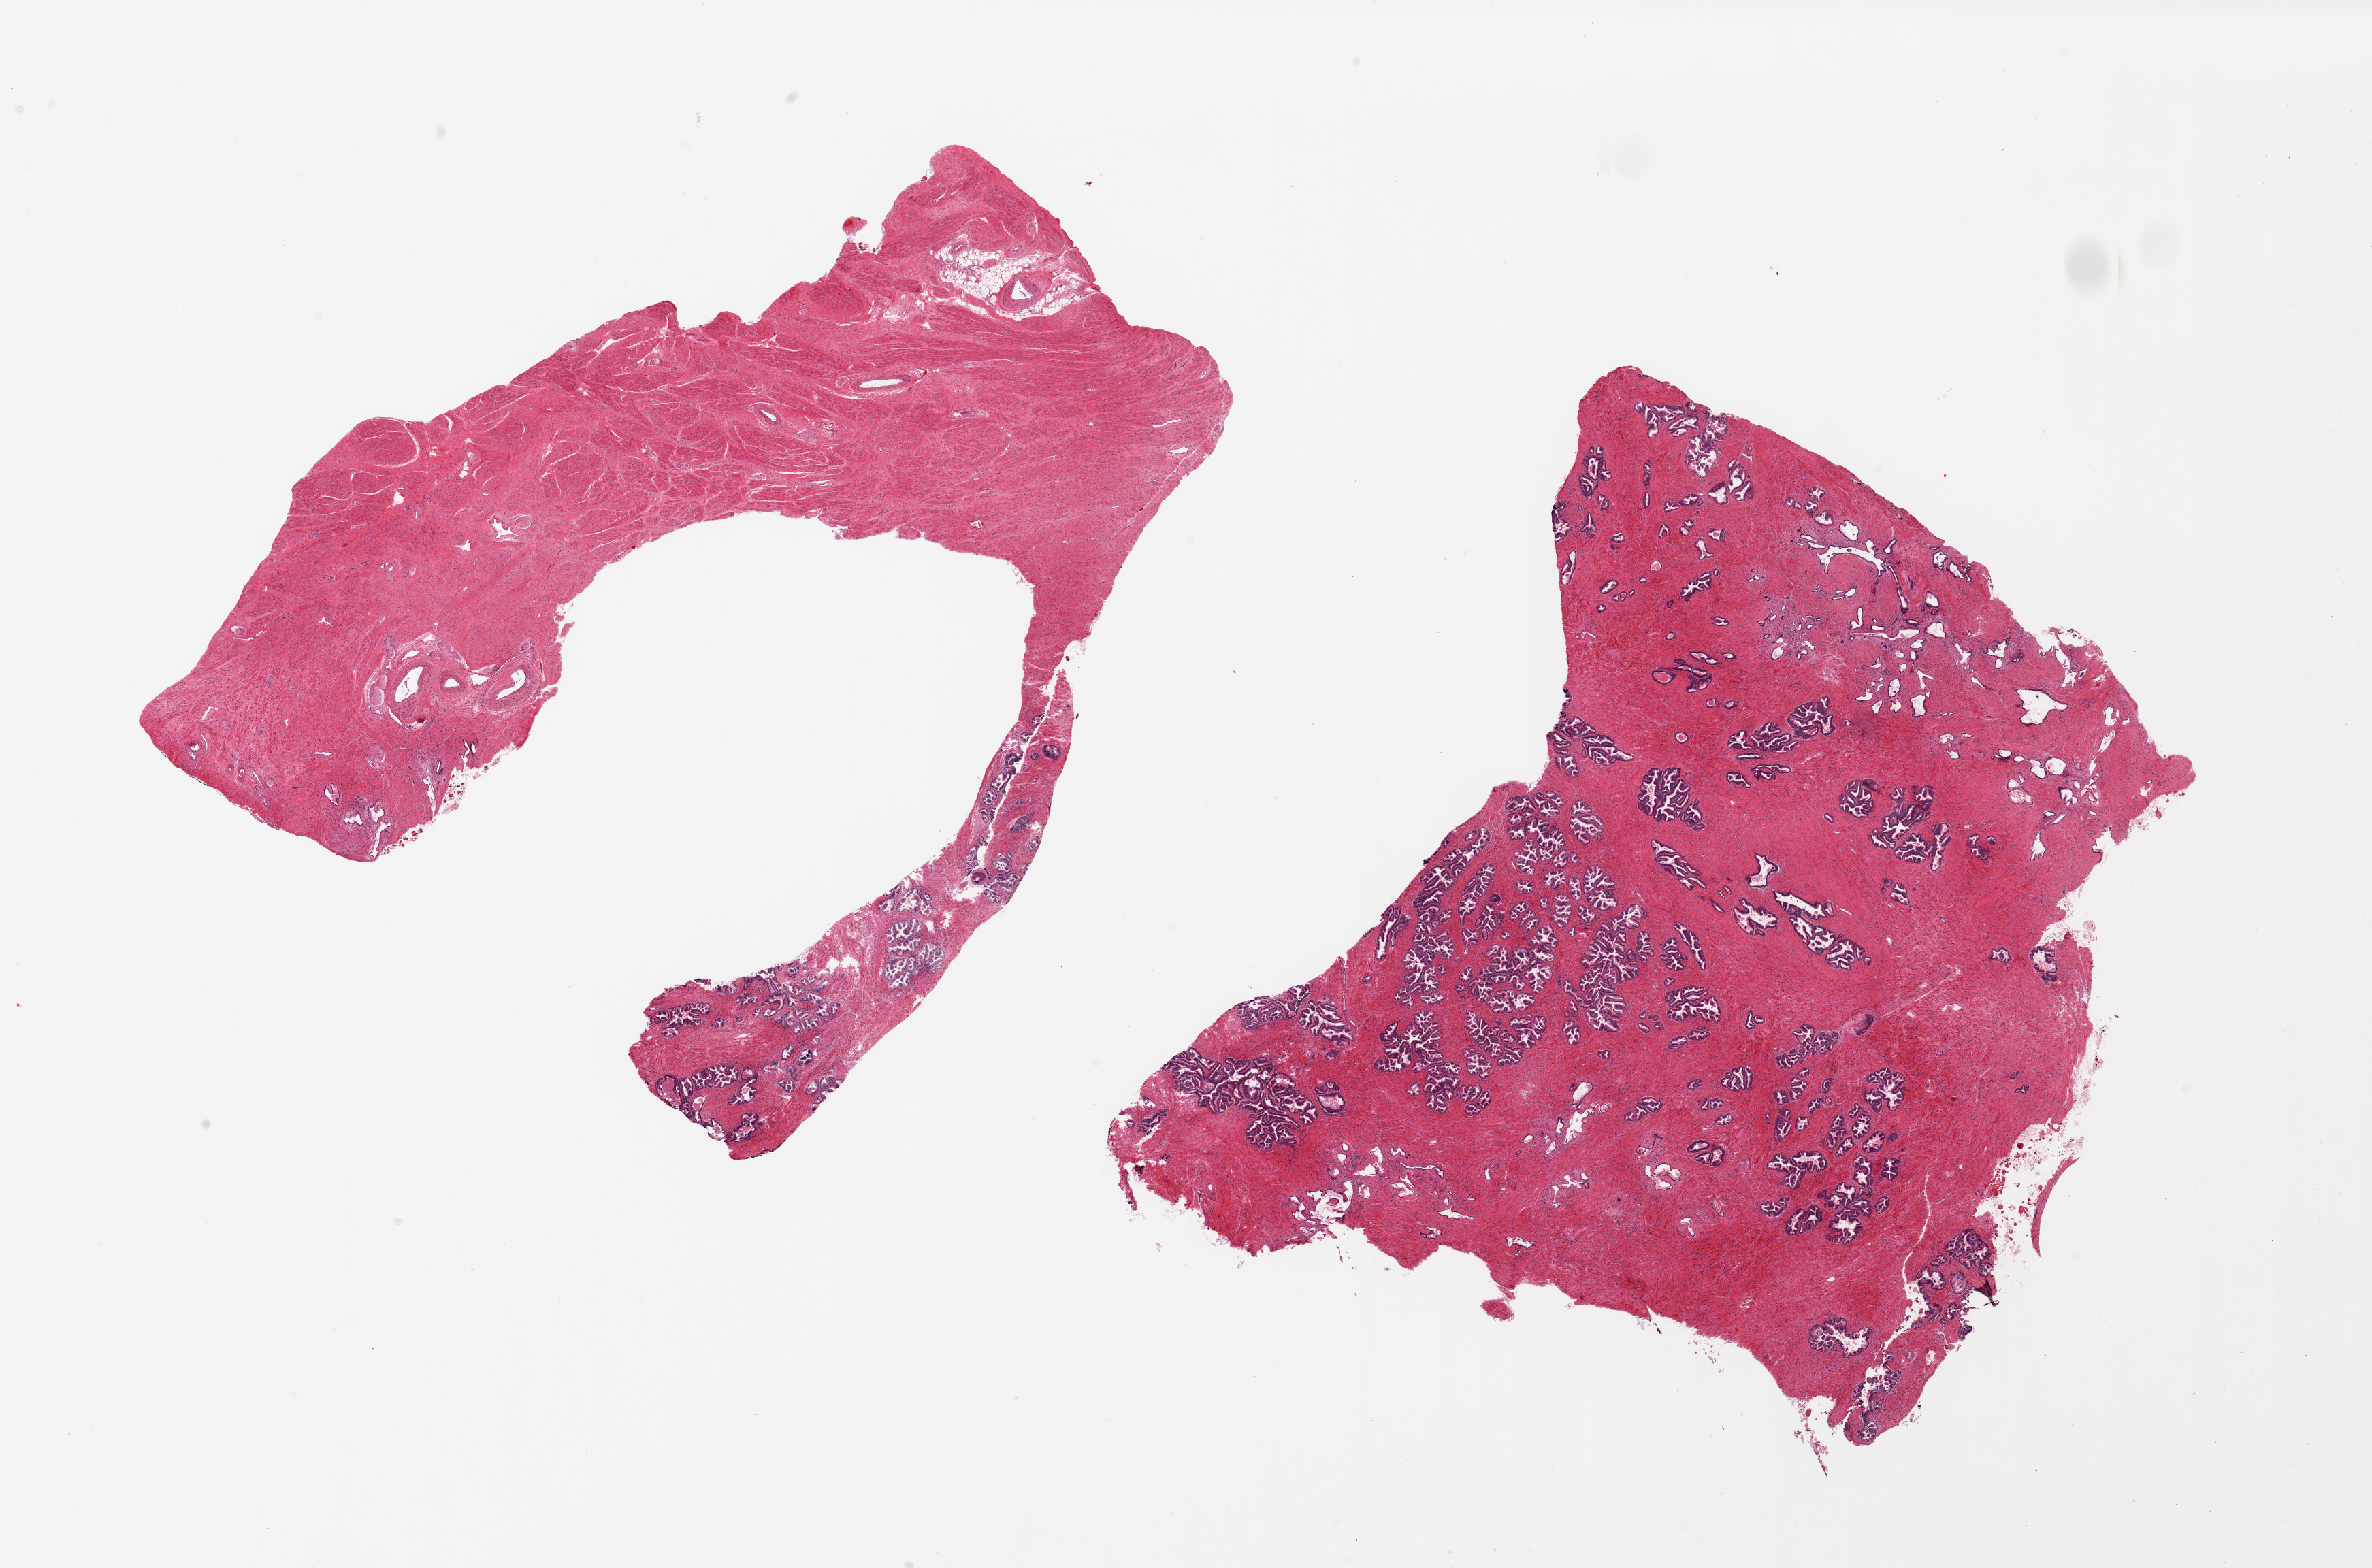
Digitized H&E-stained section, brightfield — low-resolution overview of the scanned area, about 27.6 x 18.2 mm; PAXgene-fixed paraffin-embedded (PFPE) section; section of prostate (target tissue); donor tissue sample. Donor: male.
Review note (as recorded): 2 pieces.